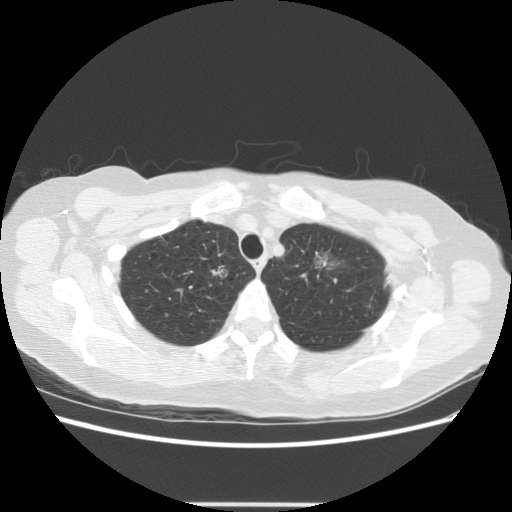
Low-dose screening chest CT, one axial slice. Slice 105 of 126 in the series (ordered by position). Reconstruction kernel STANDARD. 140 kVp. Lung window (W 1500 / L -600 HU). 512 × 512 image matrix.
Outlined on this slice (manually delineated by an expert):
- lesion 1 (tumor, upper lobe of right lung): bounding box <211,265,228,279> (left, top, right, bottom; pixels)